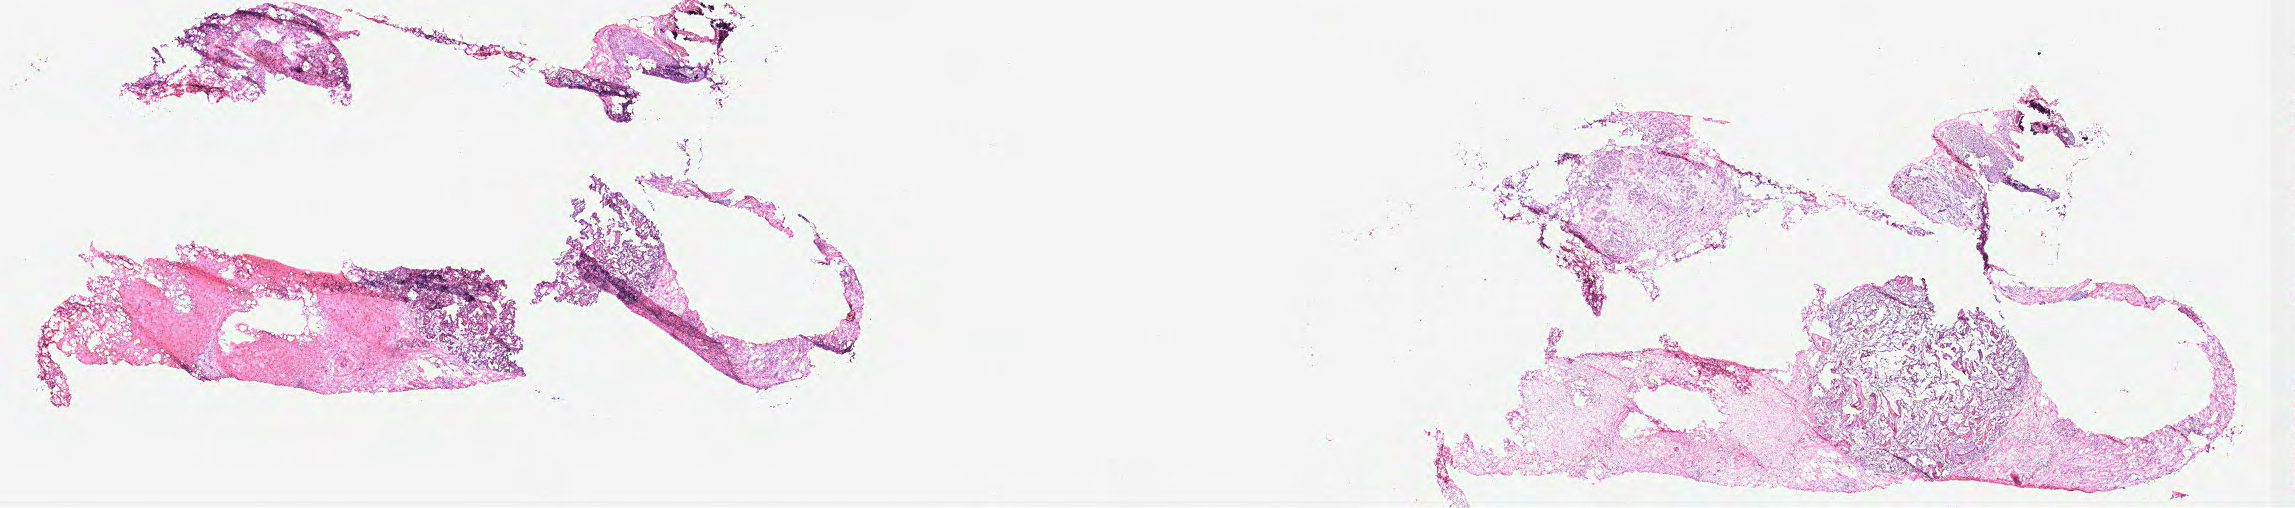
Whole-slide histology image, Hematoxylin and eosin (H&E) stained — whole scanned area (about 36.7 x 8.1 mm, from a 40x scan) shown as a low-resolution overview; breast, tissue type not recorded.
Patient diagnosis (cohort enrolment): breast cancer (breast).